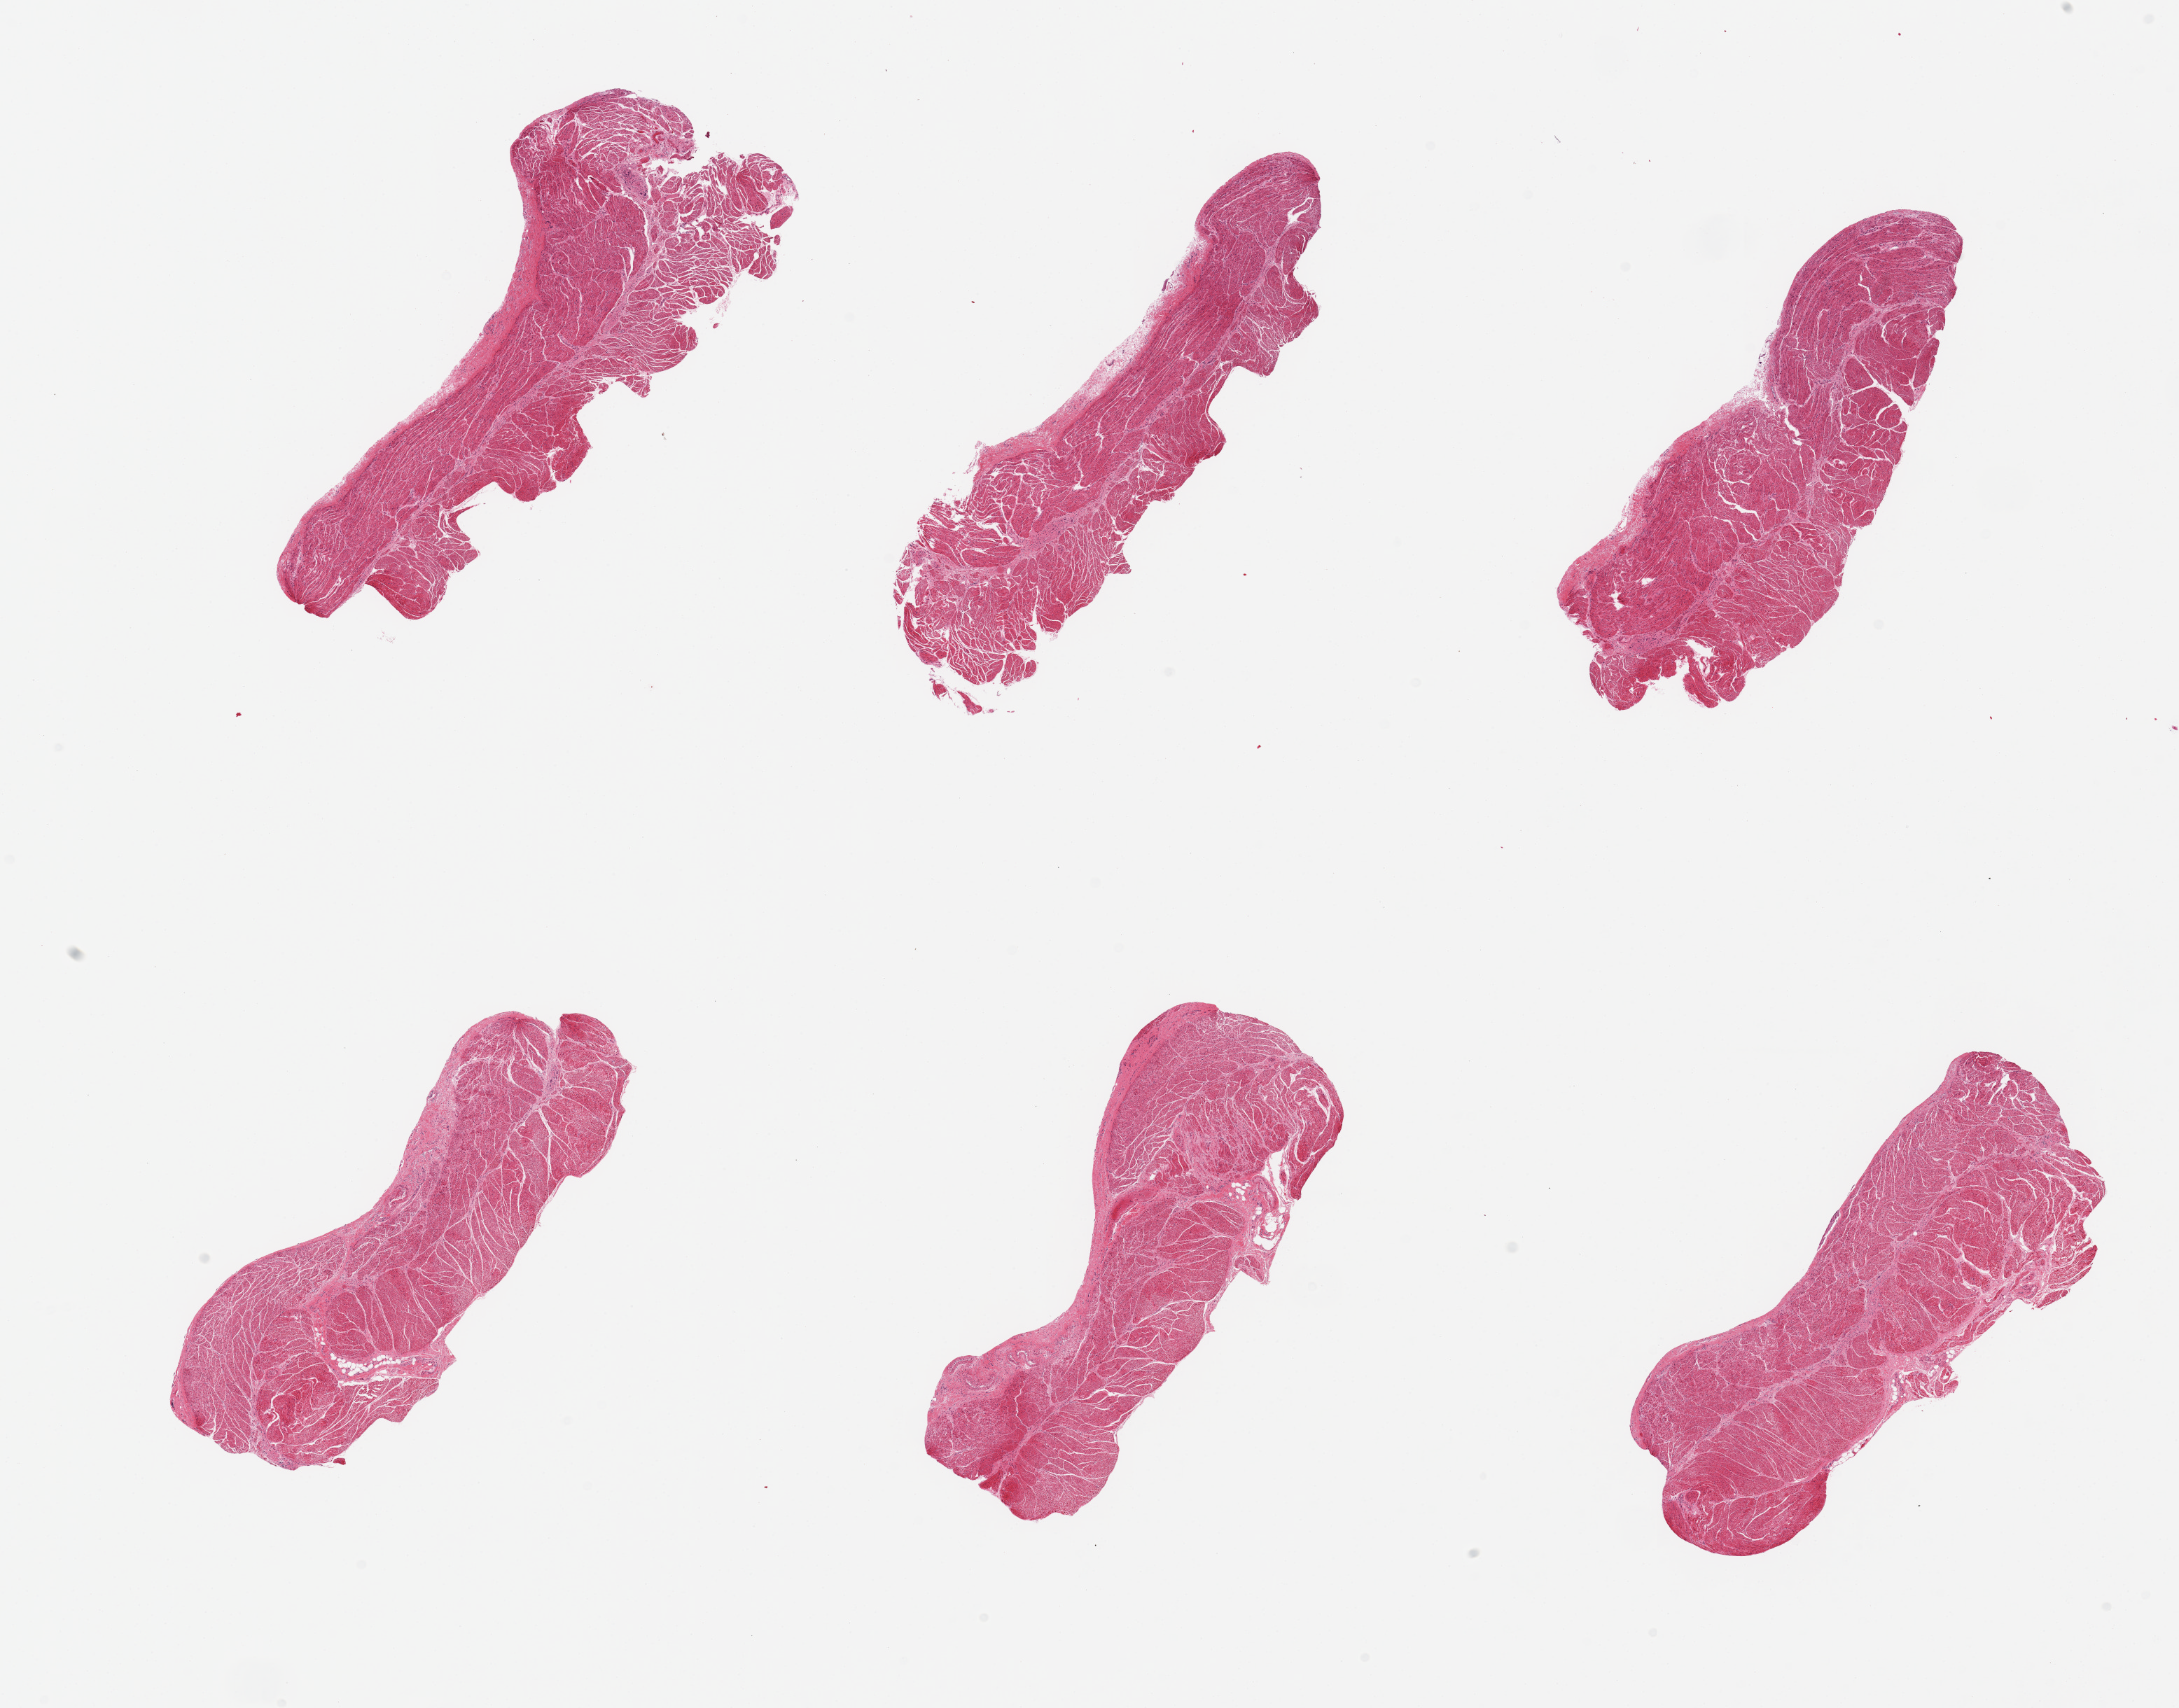
Digitized haematoxylin and eosin-stained section — low-resolution overview of the scanned area, about 24.6 x 19.3 mm (slide scanned at 20x). PAXgene-fixed, paraffin-embedded tissue. Target tissue: esophageal muscle. Donor tissue sample. Donor: male.
Review note (as recorded): 6 pieces; well trimmed.